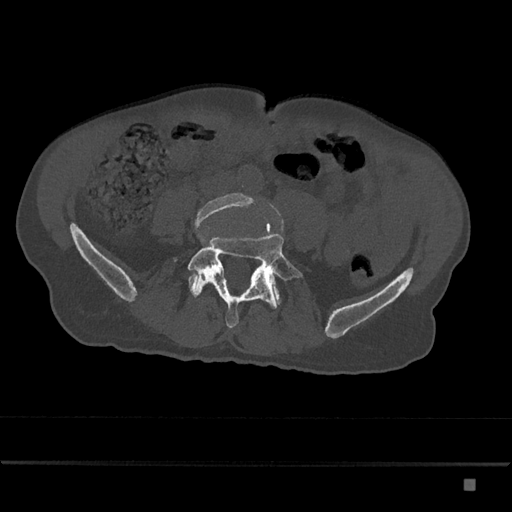
CT including the spine, one axial slice; slice 289 of 797 in the series (ordered by position); 120 kVp; bone window (W 1800 / L 400 HU); 0.5 mm slice thickness; 512 × 512 image matrix, field of view 390 × 390 mm. Patient: male, 72 years. Case-level facts recorded for this patient, not image findings: primary cancer: prostate.
Structures marked on this image (semi-automatic segmentation, software-assisted and operator-edited):
- L4 vertebra: bounding box <194,193,256,277> (left, top, right, bottom; pixels)
- L5 vertebra: <168,233,303,328>